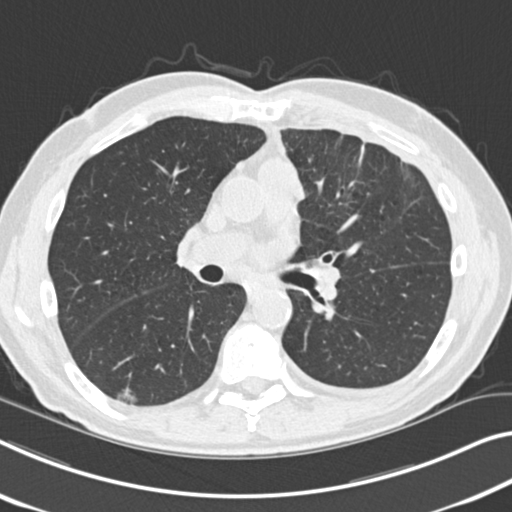
Chest CT (low-dose screening protocol), one axial image, baseline annual screen, lung window (W 1500 / L -600 HU), 2 mm slice thickness, standard (soft-tissue) reconstruction kernel (B30f), slice 103 of 212 in the series. Male participant, aged 68 years at enrolment. Current smoker at enrolment.
Expert reader's lesion annotation, bounding box (x1, y1, x2, y2) in pixels: (96, 378, 147, 416). The exam's reader record, not a measurement of the box and not confirmed to be the same lesion: non-calcified nodule or mass ≥4 mm, right lower lobe, 14 × 10 mm, poorly defined margins, ground glass attenuation. Official screen result: positive, change unspecified: nodule(s) >= 4 mm or enlarging nodule(s), mass(es), or other non-specific abnormalities suspicious for lung cancer.